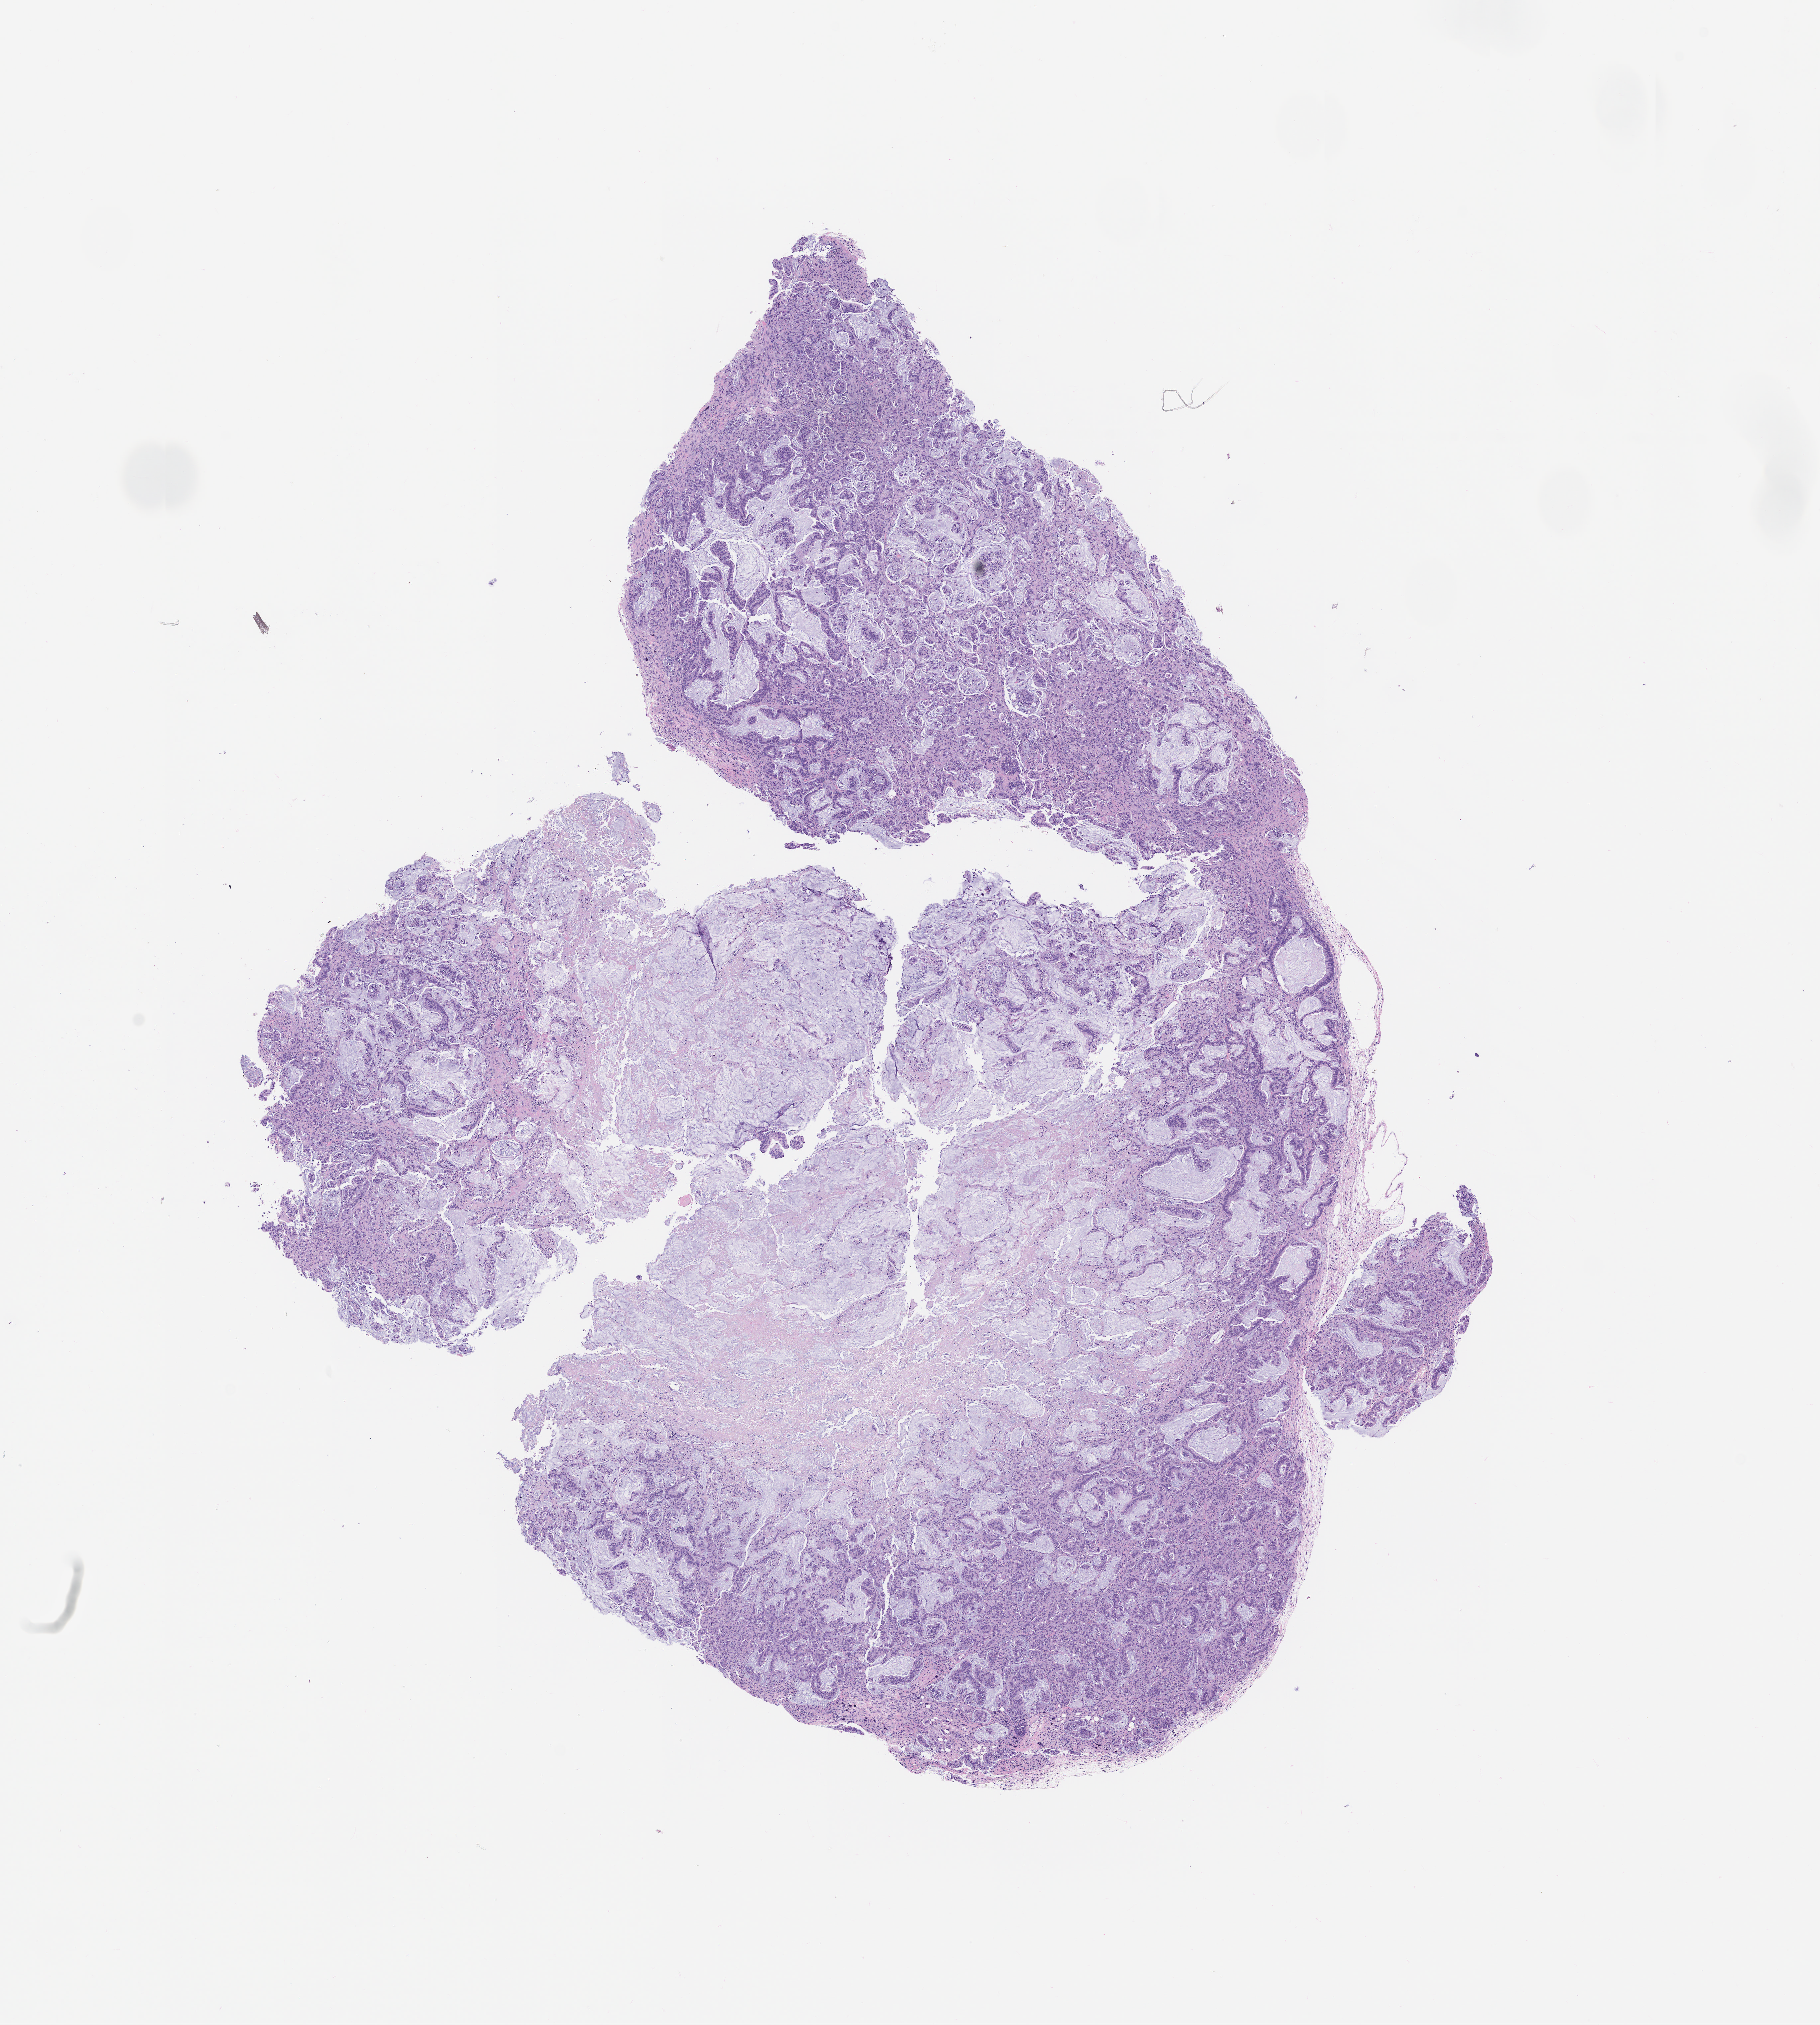
Haematoxylin and eosin whole-slide image of a patient-derived xenograft (PDX) tumor grown in a mouse, passage 1 — shown as a low-resolution overview of the whole scanned area (about 11.0 x 12.2 mm); formalin-fixed, paraffin-embedded (FFPE) tissue; tumor site category: pancreas.
Originating patient diagnosis: Pancreatic Adenocarcinoma.